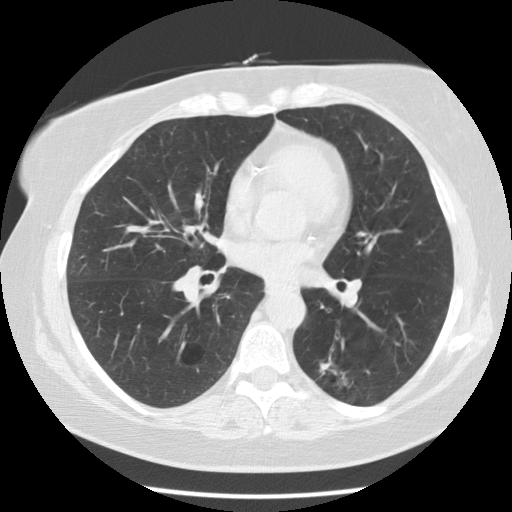
Axial slice from a low-dose chest CT screening exam, second annual screen, lung window (W 1500 / L -600 HU), slice 61 of 118 in the series, 512 × 512 image matrix. Female, age 59 years at enrolment.
- Expert-annotated lung lesion, box from (x=297, y=342) to (x=371, y=409) px.
- The screening reader recorded 5 non-calcified nodules or masses ≥4 mm on this exam (right upper lobe, right lower lobe, right lower lobe, left lower lobe, left lower lobe); which of them this box marks is not recorded.
- Official screen result: positive, other.
- Lung cancer was diagnosed 343 days after this screen (after the third annual screen): adenocarcinoma, NOS, left lower lobe, poorly differentiated (G3), stage IA (AJCC 6th edition), 15 mm at pathology.